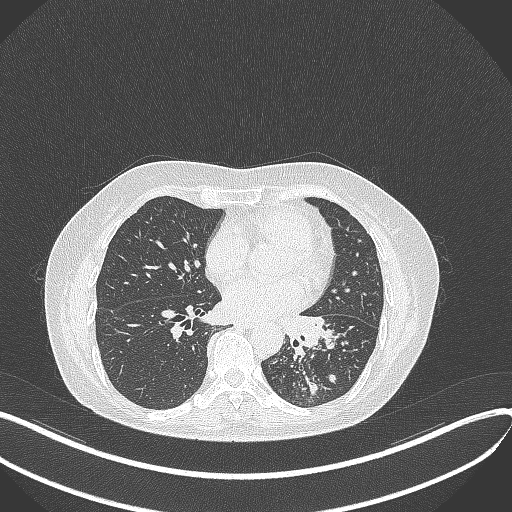
Chest CT, one axial slice; slice 181 of 429 in the series (ordered by position); reconstruction kernel B70f; lung window (W 1500 / L -600 HU); 1 mm slice thickness; 512 × 512 image matrix. Patient: female, 63 years. From the clinical record (not read from this slice): clinical TNM (as recorded): T1b N0 M0; histopathological grade: G2-3.
Annotated regions visible in this slice (rectangle marked by the reading radiologist):
- lung tumour (recorded histology: adenocarcinoma): bounding box (x1, y1, x2, y2) in pixels: (281, 309, 330, 351)